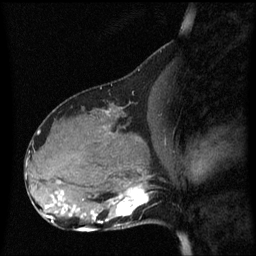
Breast MRI (dynamic contrast-enhanced), one sagittal slice; slice 26 of 60 in the series (ordered by position); dynamic contrast-enhanced series, image 2 of 3 at this slice position (ordered by acquisition); 1.5 T; TE 4.2 ms, TR 8.4 ms; 256 × 256 image matrix, field of view 210 × 210 mm. Patient: female, 31 years. Case-level facts recorded for this patient, not image findings: setting: breast cancer imaged before/during neoadjuvant chemotherapy; receptor status: HR-positive, HER2-negative.
Annotated regions visible in this slice (semi-automatically segmented with operator editing):
- analysis volume of interest (the breast-tissue region the enhancement analysis was run in; not a lesion): bounding box (x1, y1, x2, y2) in pixels: (98, 175, 158, 228)
- tumour enhancement mask (voxels above the 70 % enhancement threshold inside the analysis volume of interest): (98, 186, 150, 224)